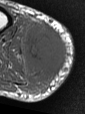
MRI of an extremity soft-tissue mass, one axial slice; slice 17 of 47 in the series (ordered by position); MR volume resampled by the dataset authors to the PET/CT grid (not the native acquisition matrix); 3.27 mm slice thickness; 85 × 114 image matrix. Male patient. From the clinical record (not read from this slice): histological type: pleiomorphic liposarcoma; grade: high; site of the primary tumour: right calf.
Annotated regions visible in this slice (expert contour drawn on MRI and transferred to this co-registered scan by the dataset authors):
- gross tumour volume including surrounding oedema: bounding box (x1, y1, x2, y2) in pixels: (22, 21, 69, 93)
- gross tumour volume (mass): (24, 27, 69, 70)